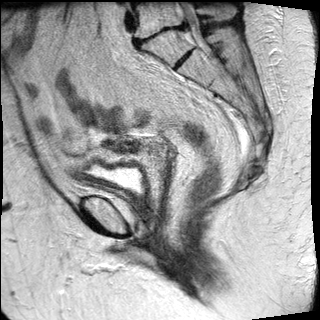
Pelvic MRI for cervical cancer, one sagittal slice; slice 16 of 27 in the series (ordered by position); T2-weighted; 1.5 T; TE 89 ms, TR 2740 ms; 4 mm slice thickness; 320 × 320 image matrix, field of view 260 × 260 mm. Female patient, age 67 years.
Annotated regions visible in this slice (expert manual segmentation):
- uterus and cervix: bounding box <106,137,135,154> (left, top, right, bottom; pixels)